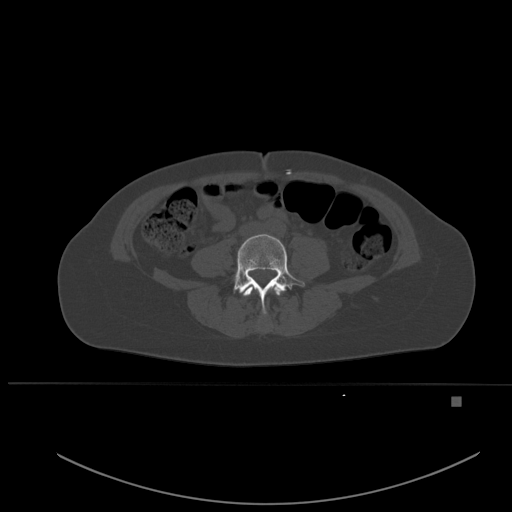
CT including the spine, one axial slice; position 176 of 651 along the scan axis; bone window (W 1800 / L 400 HU); 512 × 512 image matrix, field of view 443 × 443 mm. Female patient, age 49 years. From the clinical record (not read from this slice): primary cancer: breast.
Annotated regions visible in this slice (semi-automatically segmented with operator editing):
- L3 vertebra: box from (x=243, y=286) to (x=282, y=296) px
- L4 vertebra: (x=232, y=234)–(x=305, y=314)